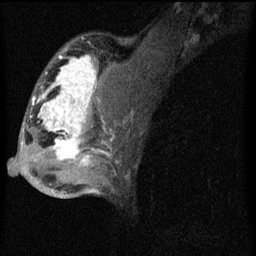
Breast MRI (dynamic contrast-enhanced), one sagittal slice. Position 36 of 60 along the scan axis. Dynamic contrast-enhanced series, image 2 of 4 at this slice position (ordered by acquisition). 1.5 T. TE 4.2 ms, TR 8 ms. 2 mm slice thickness. 256 × 256 image matrix. Patient: female, 50 years.
Structures marked on this image (semi-automatically segmented with operator editing):
- analysis volume of interest (the breast-tissue region the enhancement analysis was run in; not a lesion): bounding box (x1, y1, x2, y2) in pixels: (26, 44, 124, 177)
- tumour enhancement mask (voxels above the 70 % enhancement threshold inside the analysis volume of interest): (31, 56, 113, 165)